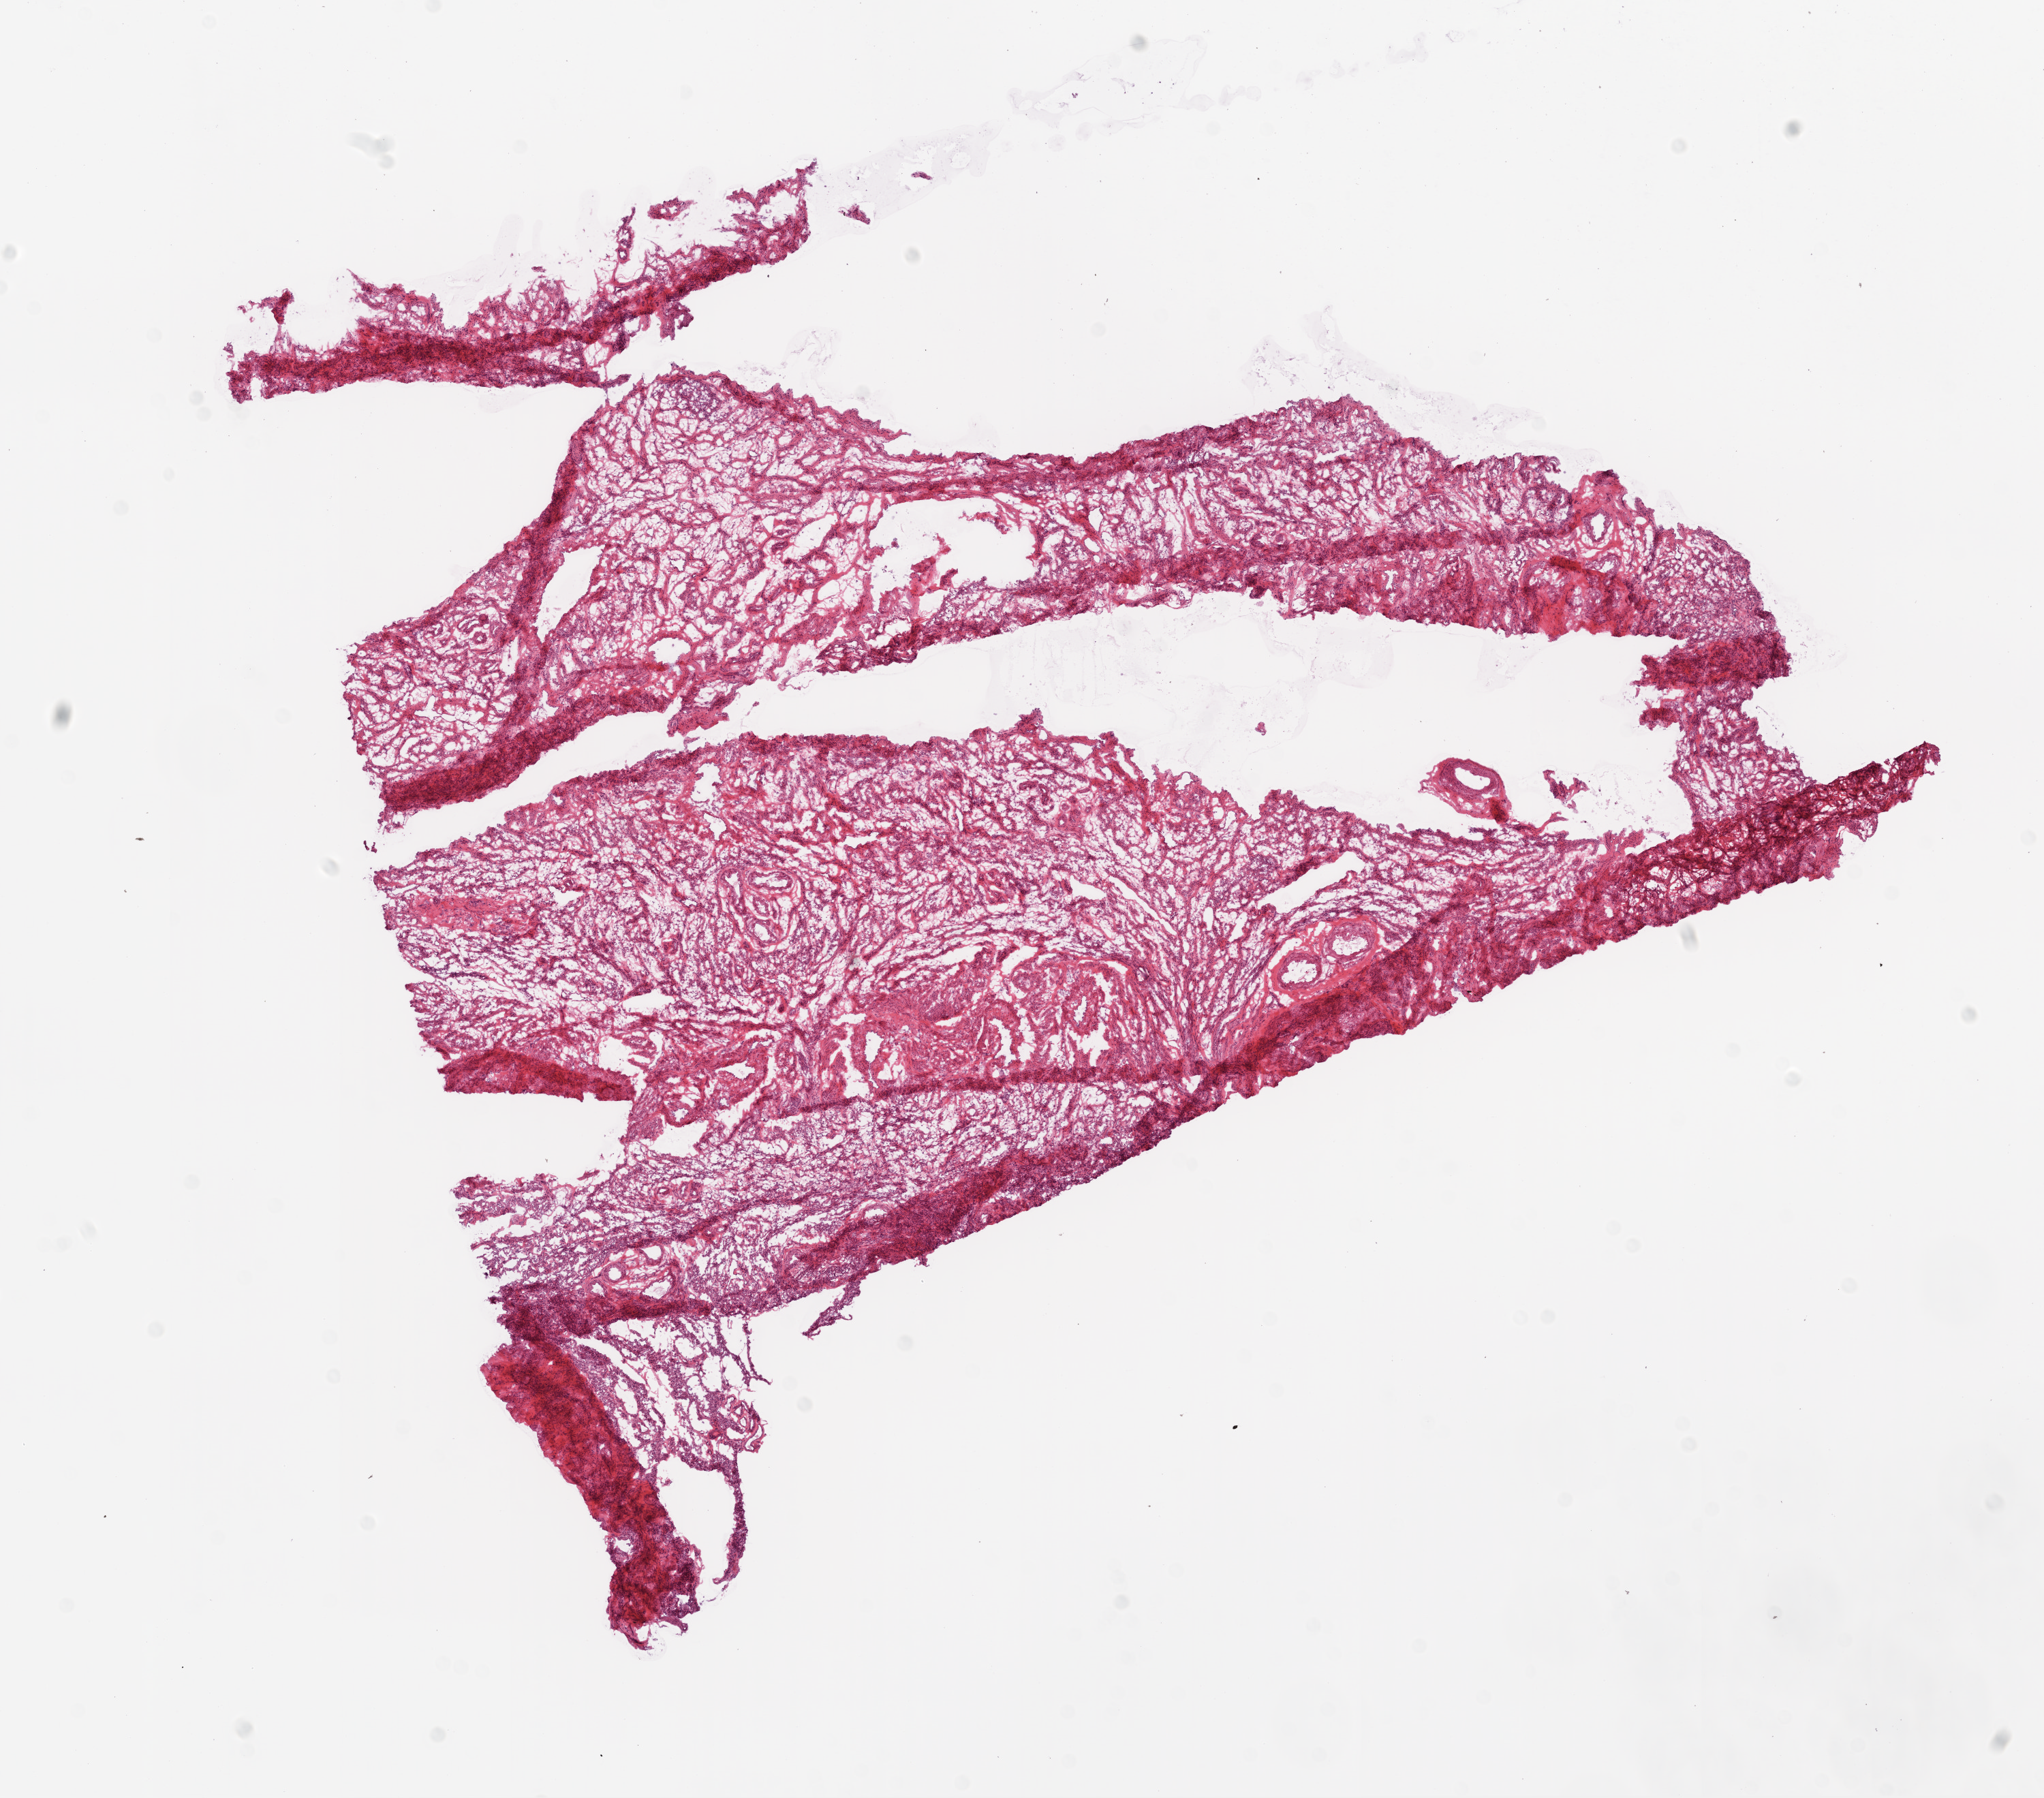
Hematoxylin and eosin (H&E) stained whole-slide image — a low-resolution overview of the entire scanned area, about 12.0 x 10.6 mm (from a 20x scan). Frozen section. Ovary, solid tissue normal (non-tumour tissue) sample. Female, age 67 years at initial diagnosis.
• this section: solid tissue normal sample (biorepository sample class)
• patient diagnosis: Serous cystadenocarcinoma, NOS